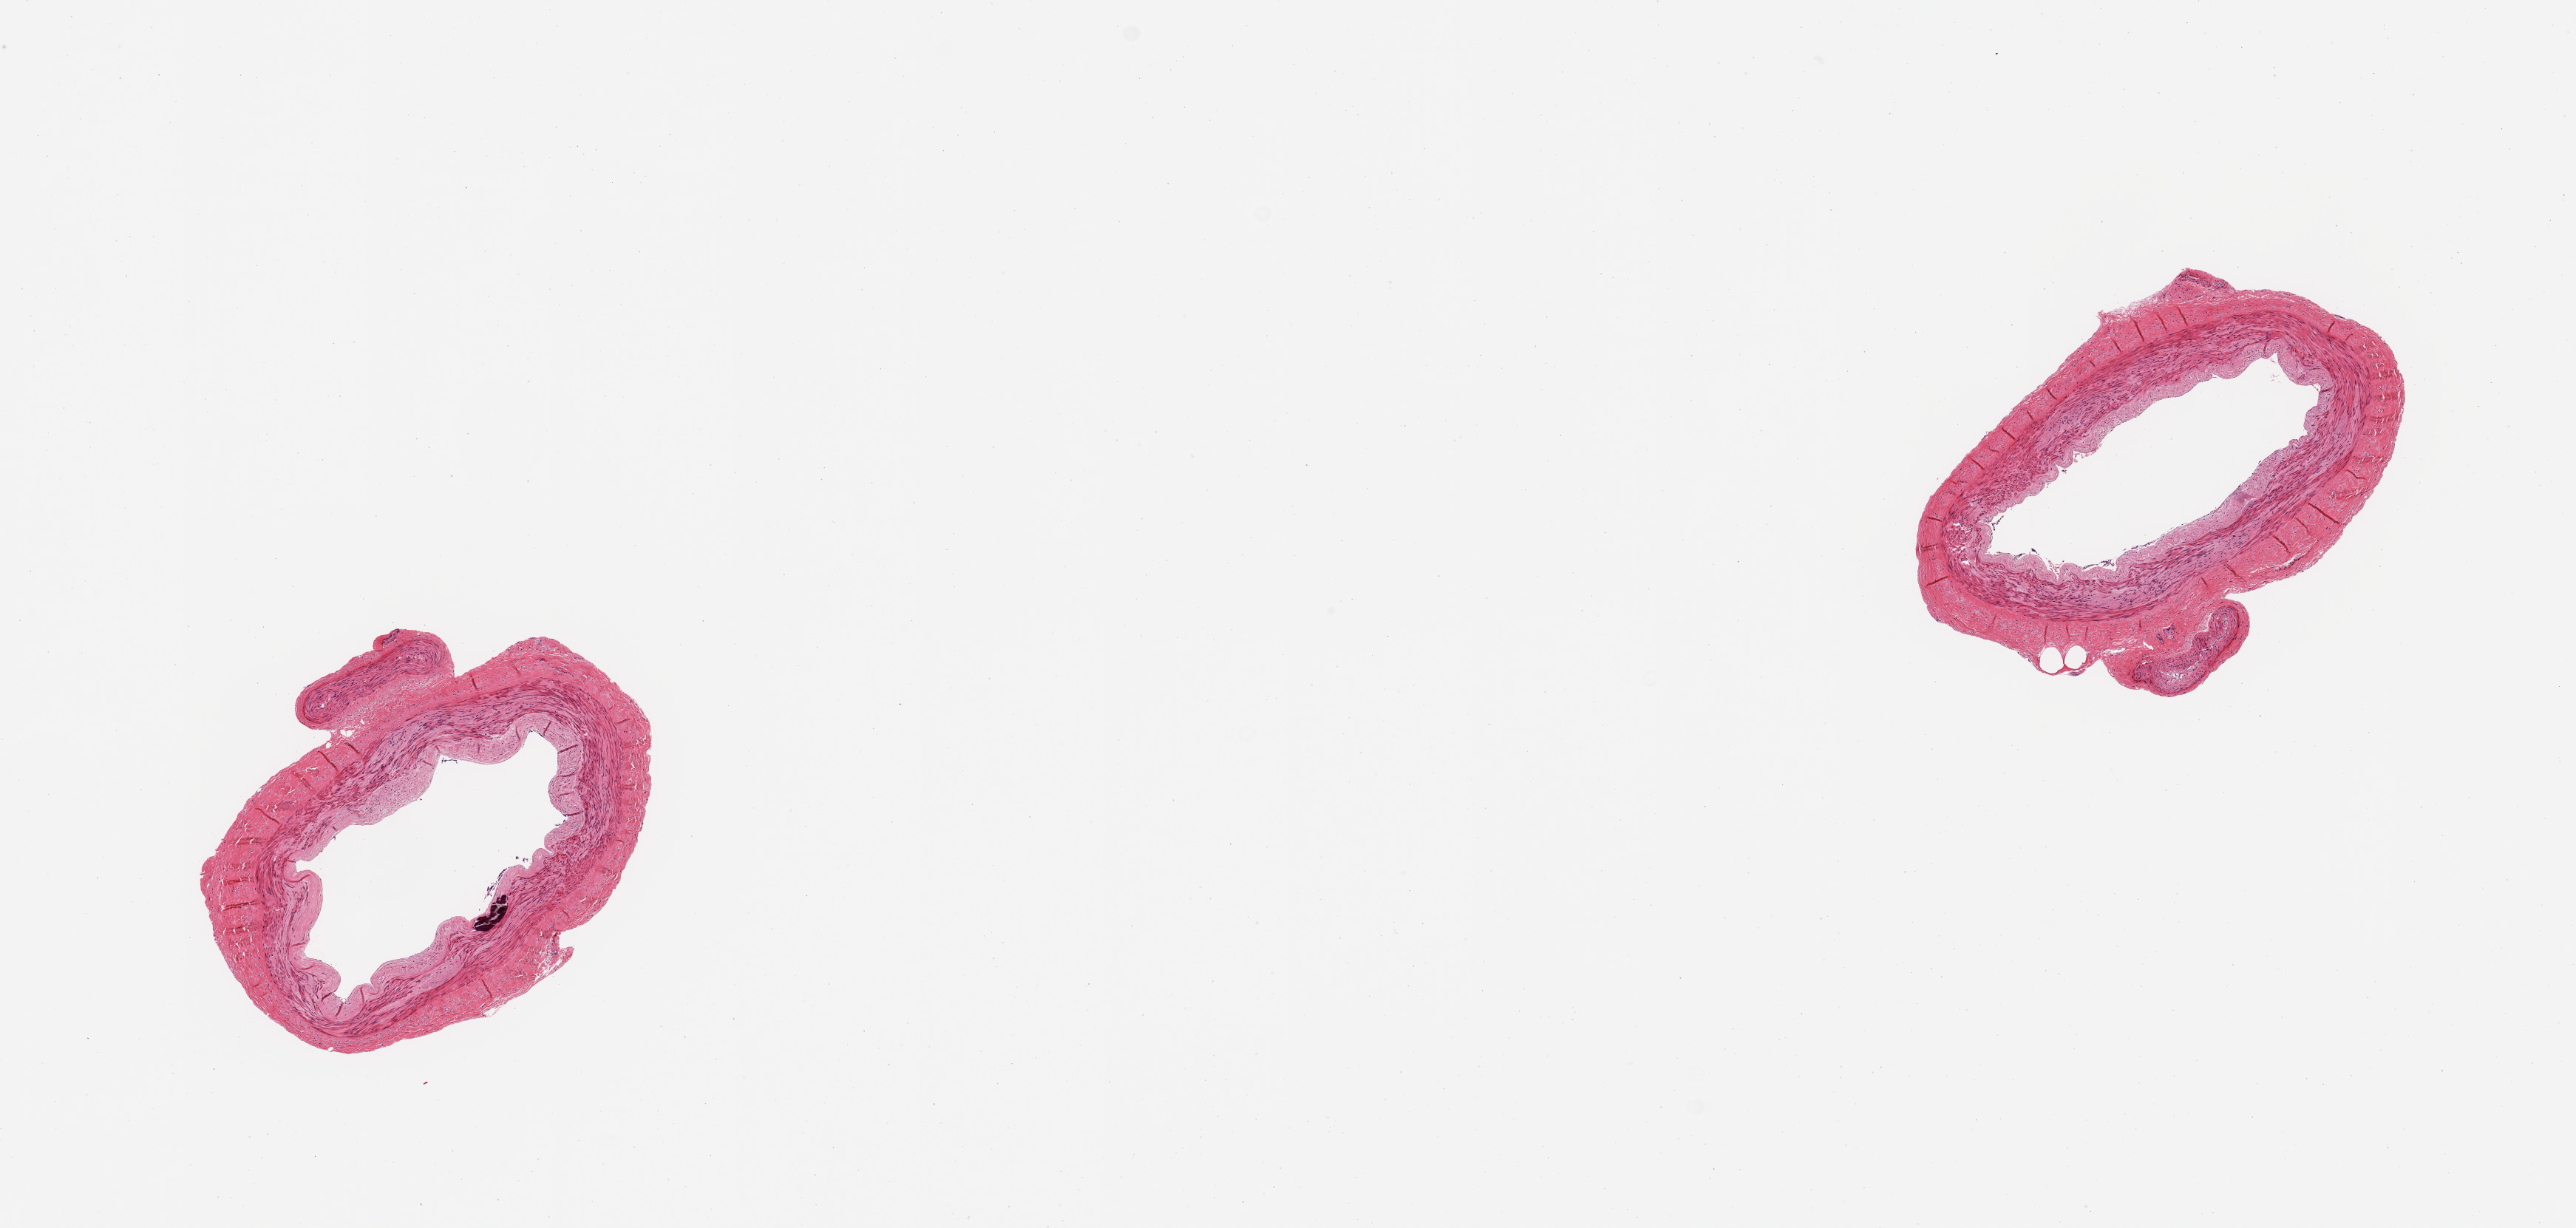
Whole-slide image, haematoxylin and eosin stain, a low-resolution overview of the entire scanned area, about 13.8 x 6.6 mm. PAXgene-fixed, paraffin-embedded tissue. Section of tibial artery (target tissue). Tissue donor sample. Donor sex: female.
Pathologist's review note for this sample: 2 pieces; mild plaque; small focal calcification; well trimmed.